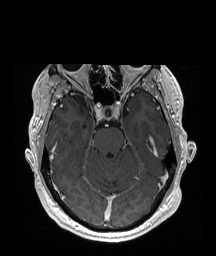
Brain MRI from a brain-tumour surgery series, one axial slice. Position 128 of 192 along the scan axis. T1-weighted post-contrast. 1 mm slice thickness. 216 × 256 image matrix, field of view 219 × 260 mm. Case-level facts recorded for this patient, not image findings: histopathology: Astrocytoma; WHO grade: 2; IDH mutation: yes.
Outlined on this slice (expert manual segmentation):
- tumour: box from (x=70, y=95) to (x=90, y=112) px